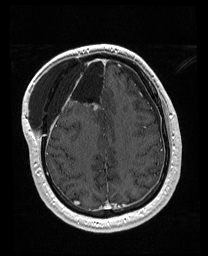
Brain MRI from a brain-tumour surgery series, one axial slice; position 58 of 176 along the scan axis; T1-weighted post-contrast; 1 mm slice thickness; 208 × 256 image matrix, field of view 208 × 256 mm. From the clinical record (not read from this slice): histopathology: Astrocytoma; WHO grade: 4; IDH mutation: yes; tumour location: Right Orbitofrontal Anterior Temporal Insular.
Outlined on this slice (outlined manually by an expert reader):
- previous resection cavity: bounding box (x1, y1, x2, y2) in pixels: (56, 55, 106, 101)